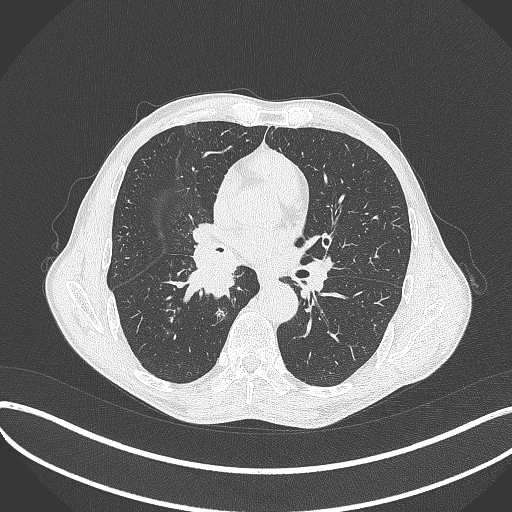
Chest CT, one axial slice. Slice 225 of 481 in the series (ordered by position). Reconstruction kernel B70f. Lung window (W 1500 / L -600 HU). 1 mm slice thickness. 512 × 512 image matrix, field of view 400 × 400 mm. Patient: male, 65 years. From the clinical record (not read from this slice): clinical TNM (as recorded): T2a N0 M0.
Structures marked on this image (bounding box drawn by a radiologist):
- lung tumour (recorded histology: squamous cell carcinoma): bounding box (x1, y1, x2, y2) in pixels: (177, 228, 240, 305)